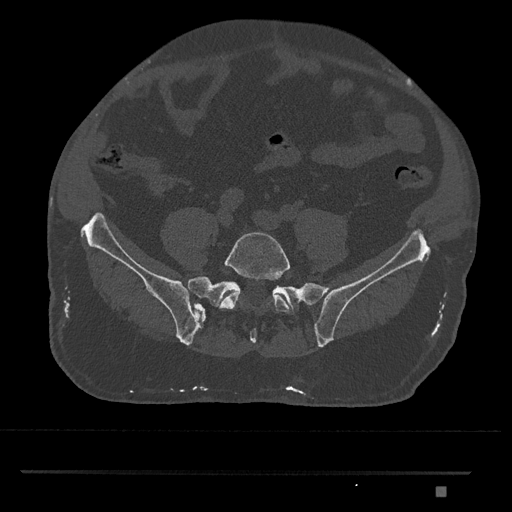
CT including the spine, one axial slice. Slice 536 of 1134 in the series (ordered by position). Reconstruction kernel Br40s/3. Bone window (W 1800 / L 400 HU). 512 × 512 image matrix, field of view 429 × 429 mm. Male patient, age 65 years. Case-level facts recorded for this patient, not image findings: primary cancer: prostate.
Annotated regions visible in this slice (semi-automatically segmented with operator editing):
- L5 vertebra: box from (x=219, y=231) to (x=291, y=314) px